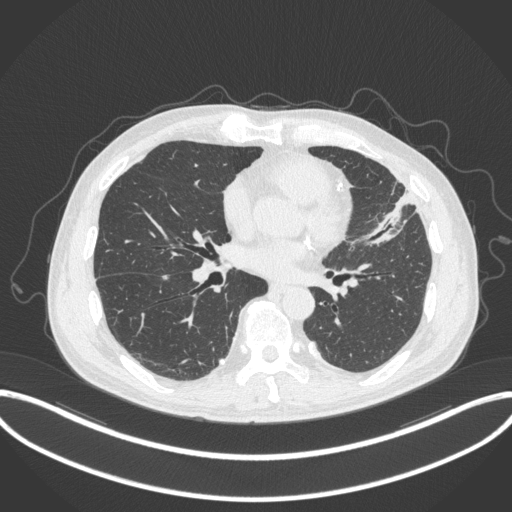
Chest CT, one axial slice. Slice 151 of 382 in the series (ordered by position). Reconstruction kernel B31f. 120 kVp. Lung window (W 1500 / L -600 HU). 512 × 512 image matrix, field of view 415 × 415 mm. Patient: male, 64 years. Case-level facts recorded for this patient, not image findings: clinical TNM (as recorded): T4 N1 M0.
Outlined on this slice (rectangle marked by the reading radiologist):
- lung tumour (recorded histology: adenocarcinoma): bounding box [x1, y1, x2, y2] px = [366, 189, 415, 248]